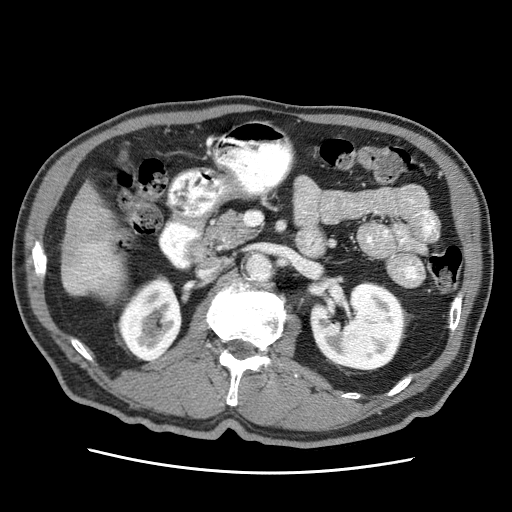
Contrast-enhanced abdominal CT (liver protocol), one axial slice. Reconstruction kernel STANDARD. 120 kVp. Soft-tissue window (W 400 / L 40 HU). 2.5 mm slice thickness. 512 × 512 image matrix, field of view 360 × 360 mm. From the clinical record (not read from this slice): diagnosis: hepatocellular carcinoma (patient treated with transarterial chemoembolisation; whether this scan precedes or follows treatment is not stated here); TNM stage (as recorded): Stage-IIIA; Child-Pugh class: A; tumour differentiation: well differentiated.
Structures marked on this image (semi-automatic segmentation, software-assisted and operator-edited):
- liver parenchyma outside the tumour (the mass and vessels are separate outlines, so this box may not span the whole liver): bounding box (x1, y1, x2, y2) in pixels: (62, 184, 122, 294)
- liver vessels: (84, 244, 110, 279)